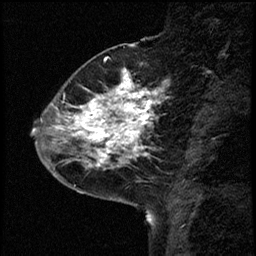
Breast MRI (dynamic contrast-enhanced), one sagittal slice. Slice 18 of 68 in the series (ordered by position). Dynamic contrast-enhanced study with each time point stored as its own series, time point 2 of 3 at this slice position (early post-contrast, ordered by acquisition time). 1.5 T. TE 4.2 ms, TR 17.6 ms. 2 mm slice thickness. 256 × 256 image matrix. Patient: female, 52 years. Case-level facts recorded for this patient, not image findings: setting: breast cancer imaged before/during neoadjuvant chemotherapy; receptor status: HER2-positive.
Structures marked on this image (semi-automatic segmentation, software-assisted and operator-edited):
- analysis volume of interest (the breast-tissue region the enhancement analysis was run in; not a lesion): bounding box [x1, y1, x2, y2] px = [50, 61, 169, 184]
- tumour enhancement mask (voxels above the 100 % enhancement threshold inside the analysis volume of interest): [50, 73, 161, 175]